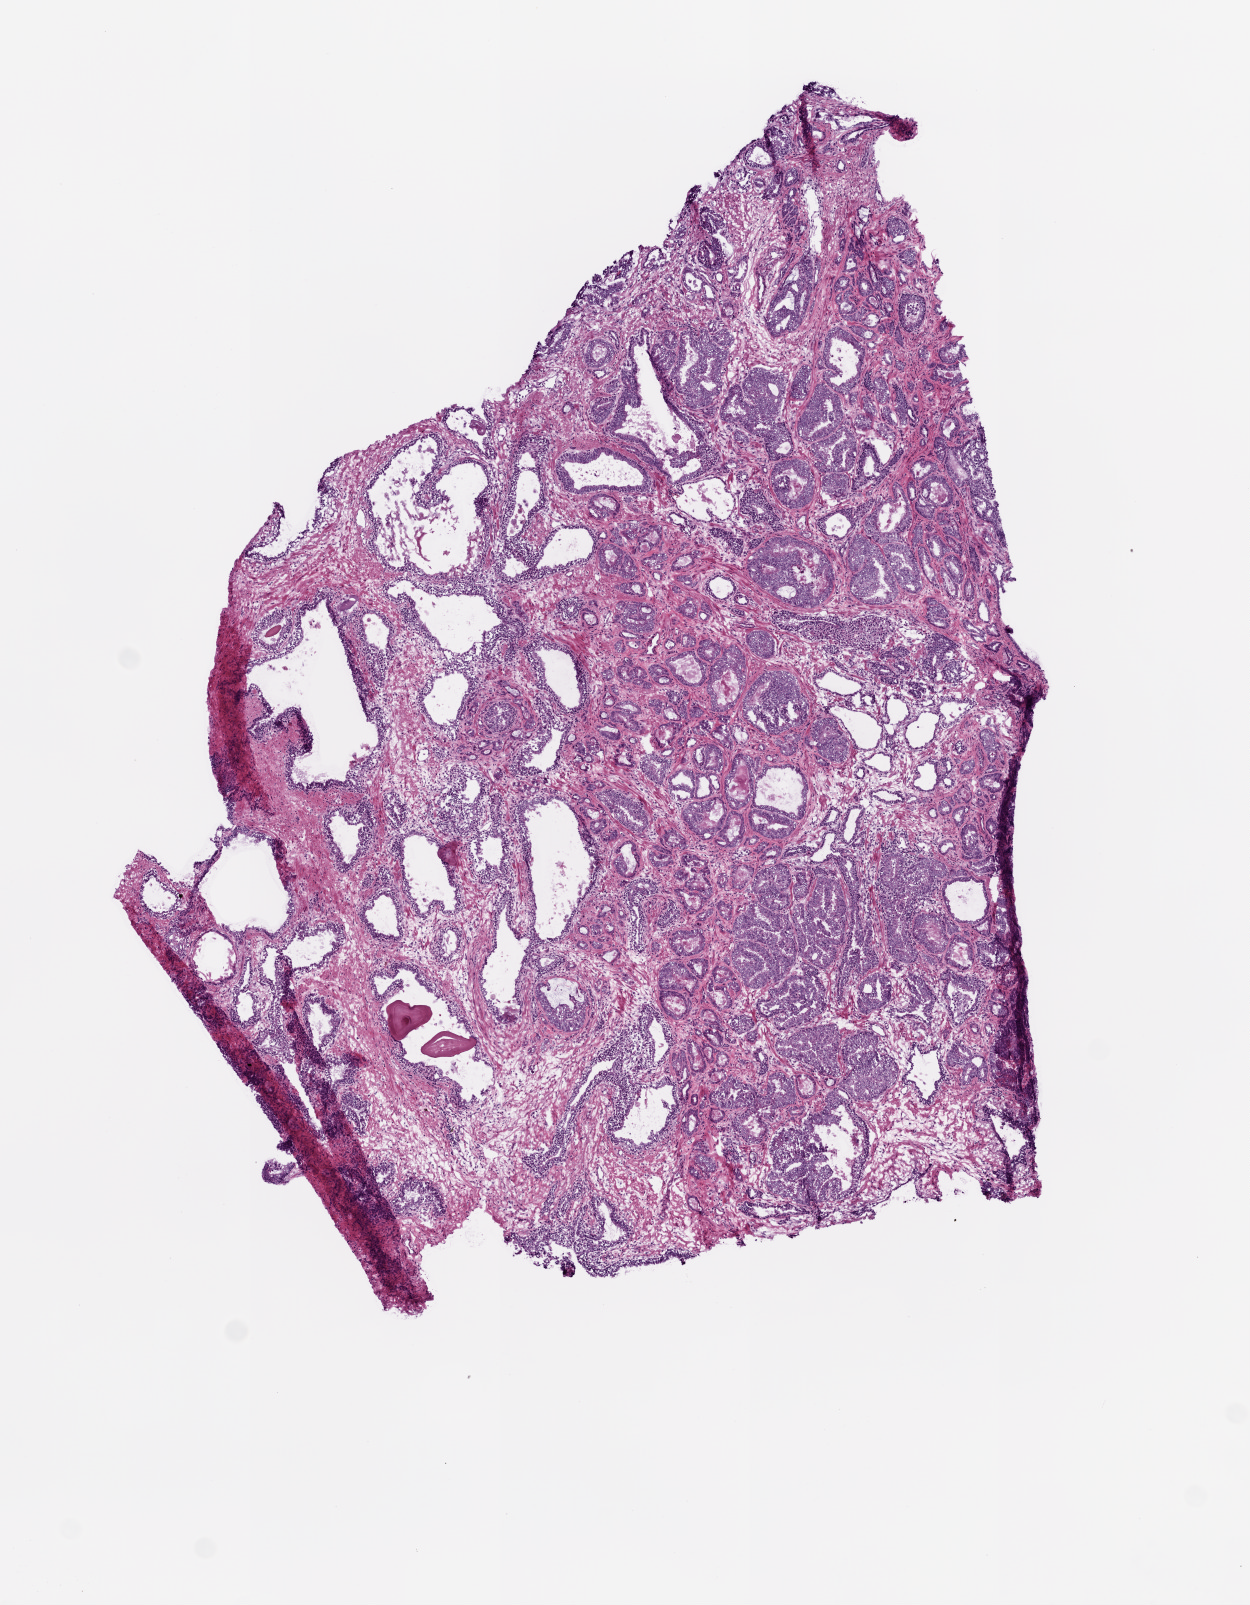
Whole-slide histology image, Hematoxylin and eosin (H&E) stained, low-resolution overview of the scanned area, about 5.0 x 6.4 mm (slide scanned at 20x); frozen section; prostate, primary tumour sample. Male patient; age at initial diagnosis 66 years. Gleason score: 7 (3+4). Composition of this section per pathologist review: tumour cells 50%, tumour nuclei 60%, normal cells 25%, stromal cells 25%, necrosis 0%. Infiltration values recorded for this section: lymphocyte infiltration 1%, monocyte infiltration 0%, neutrophil infiltration 0%.
• lymph nodes positive (case pathology): 0 of 1 examined
• pathologic diagnosis: Acinar cell carcinoma (prostate gland)